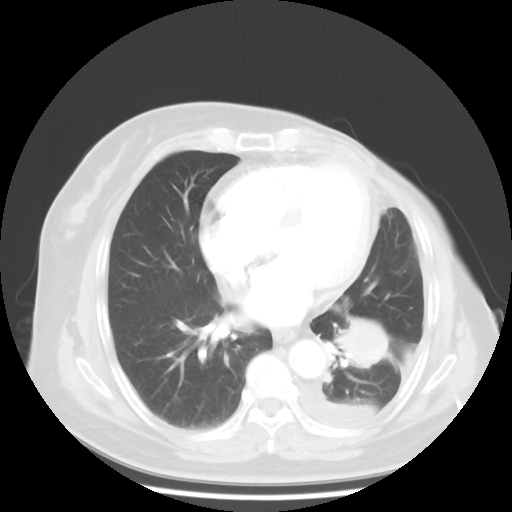
Chest CT, one axial slice; slice 18 of 48 in the series (ordered by position); lung window (W 1500 / L -600 HU); 5 mm slice thickness; 512 × 512 image matrix, field of view 360 × 360 mm. Female patient, age 63 years. From the clinical record (not read from this slice): clinical TNM (as recorded): T2 N0 M1.
Annotated regions visible in this slice (bounding box drawn by a radiologist):
- lung tumour (recorded histology: adenocarcinoma): bounding box (x1, y1, x2, y2) in pixels: (332, 307, 387, 376)